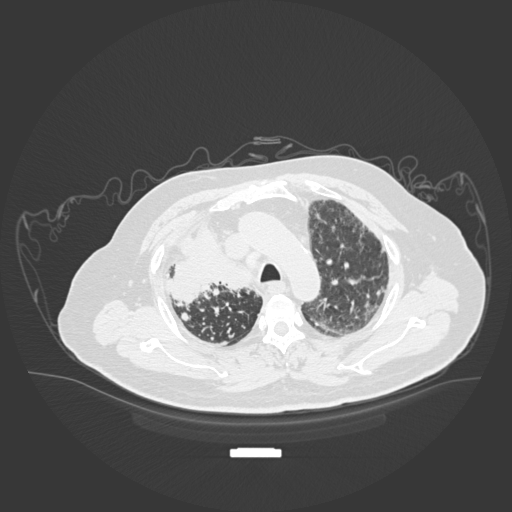
Chest CT, one axial slice; slice 139 of 201 in the series (ordered by position); reconstruction kernel B30f; 120 kVp; lung window (W 1500 / L -600 HU); 1 mm slice thickness; 512 × 512 image matrix, field of view 500 × 500 mm. Patient: male, 69 years. From the clinical record (not read from this slice): clinical TNM (as recorded): T4 N3 M1.
Annotated regions visible in this slice (rectangle marked by the reading radiologist):
- lung tumour (recorded histology: adenocarcinoma): box from (x=162, y=223) to (x=256, y=305) px